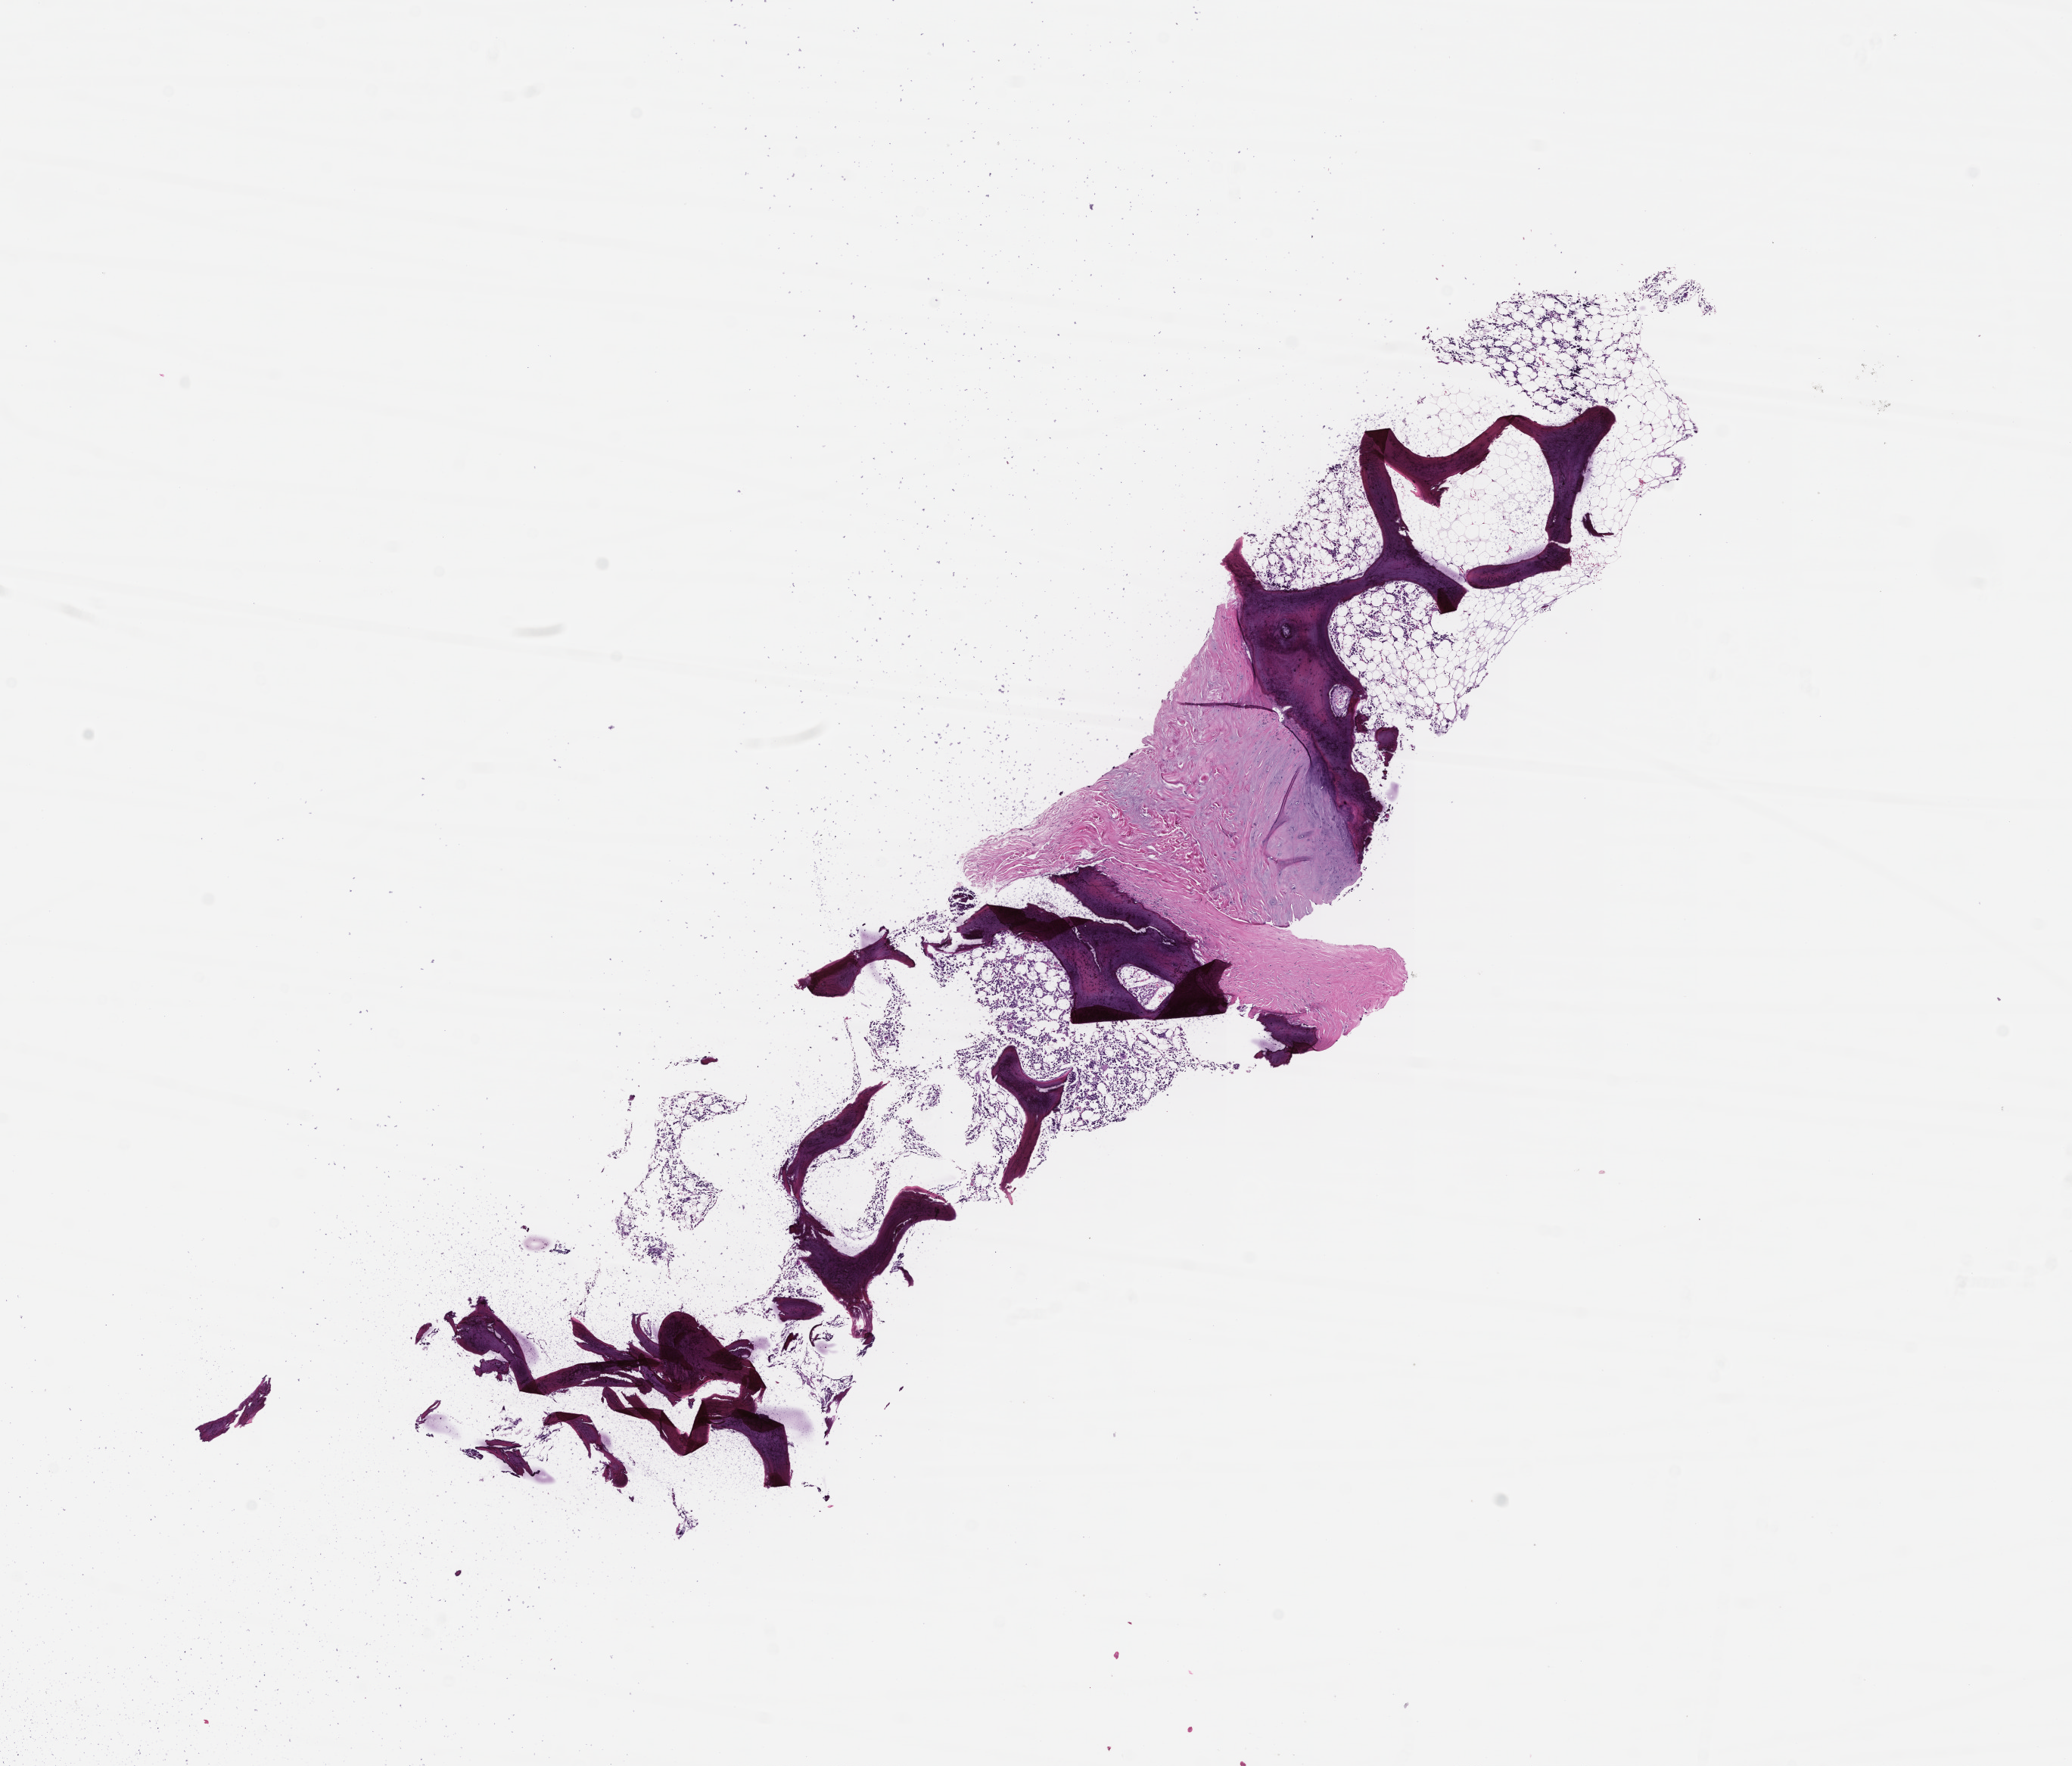
H&E whole-slide image, a low-resolution overview of the entire scanned area, about 11.1 x 9.4 mm. FFPE section. Site: bone marrow. Specimen time point: collected on treatment. Female patient.
This section: primary tumor. Diagnosis: Plasma Cell Myeloma.